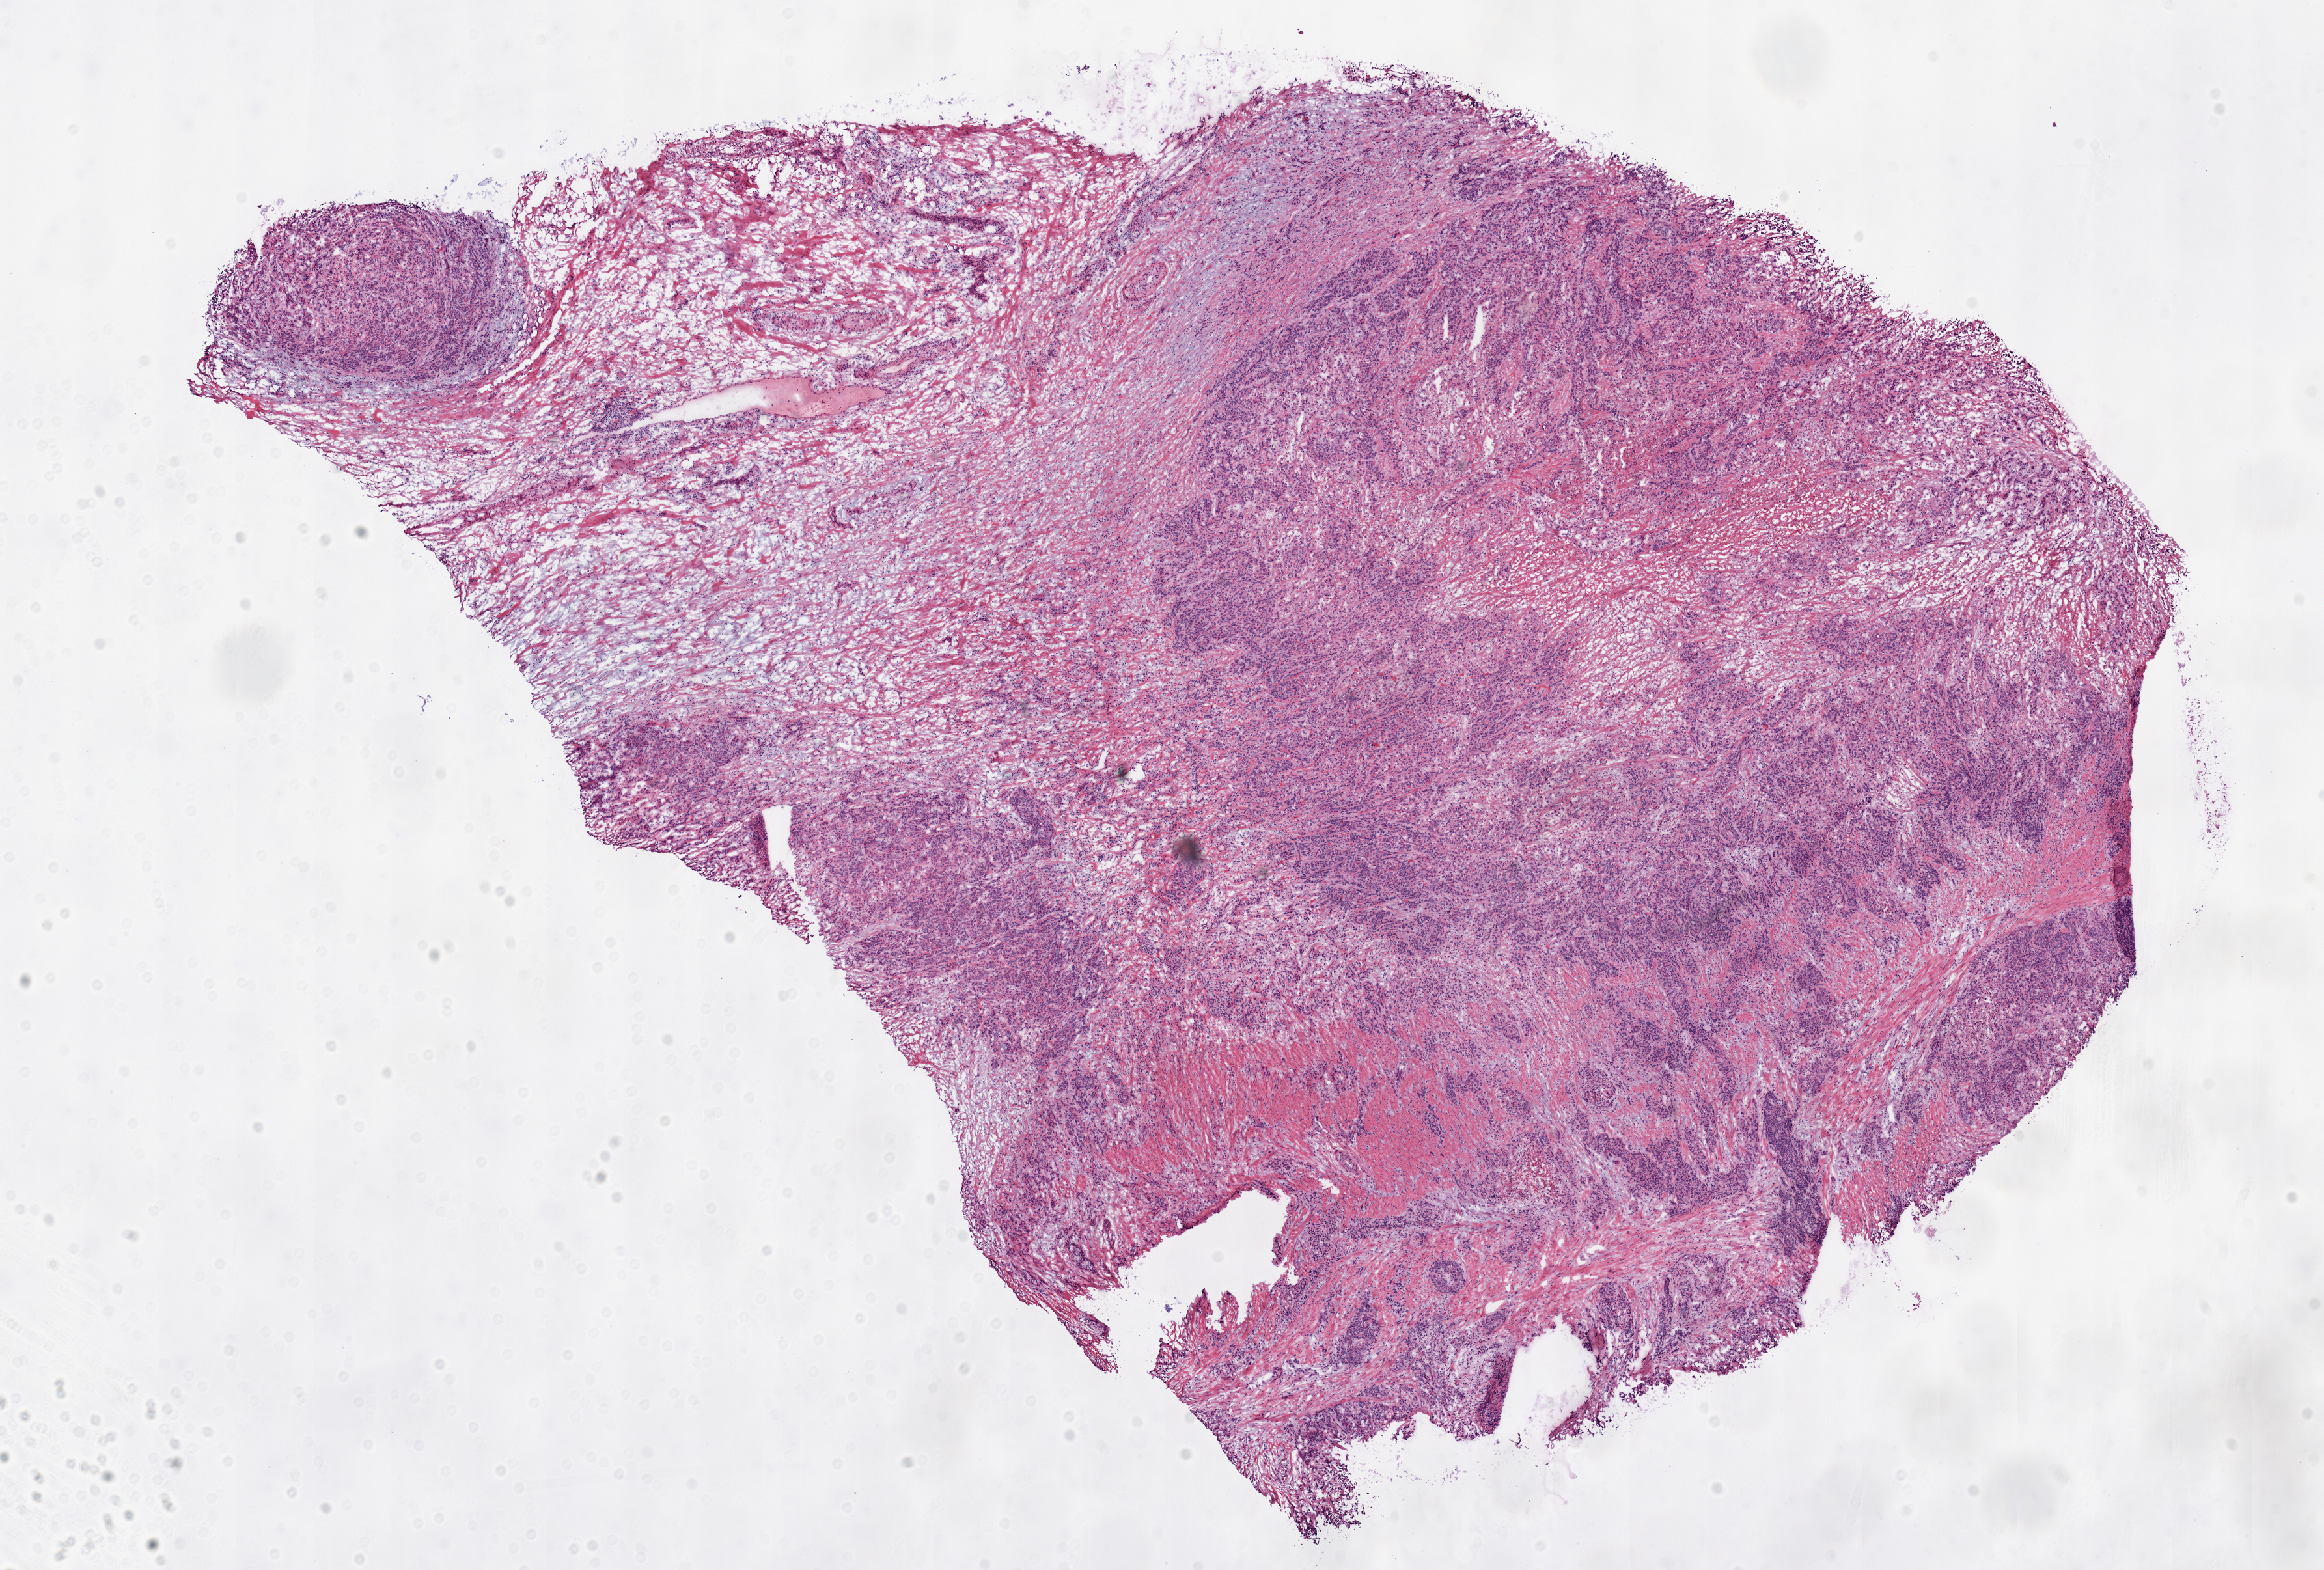
Digitized H&E-stained tissue section (whole slide) — shown as a low-resolution overview of the whole scanned area (about 14.2 x 9.6 mm, from a 20x scan), frozen section from the top of the tissue portion, sample: primary tumour, stomach. Male patient; age at initial diagnosis 45 years. Histologic grade: G3 (poorly differentiated). Composition of this section per pathologist review: tumour cells 80%, tumour nuclei 80%, normal cells 0%, stromal cells 20%, necrosis 0%.
Pathologic diagnosis: Adenocarcinoma, intestinal type (gastric antrum). AJCC pathologic stage: II.